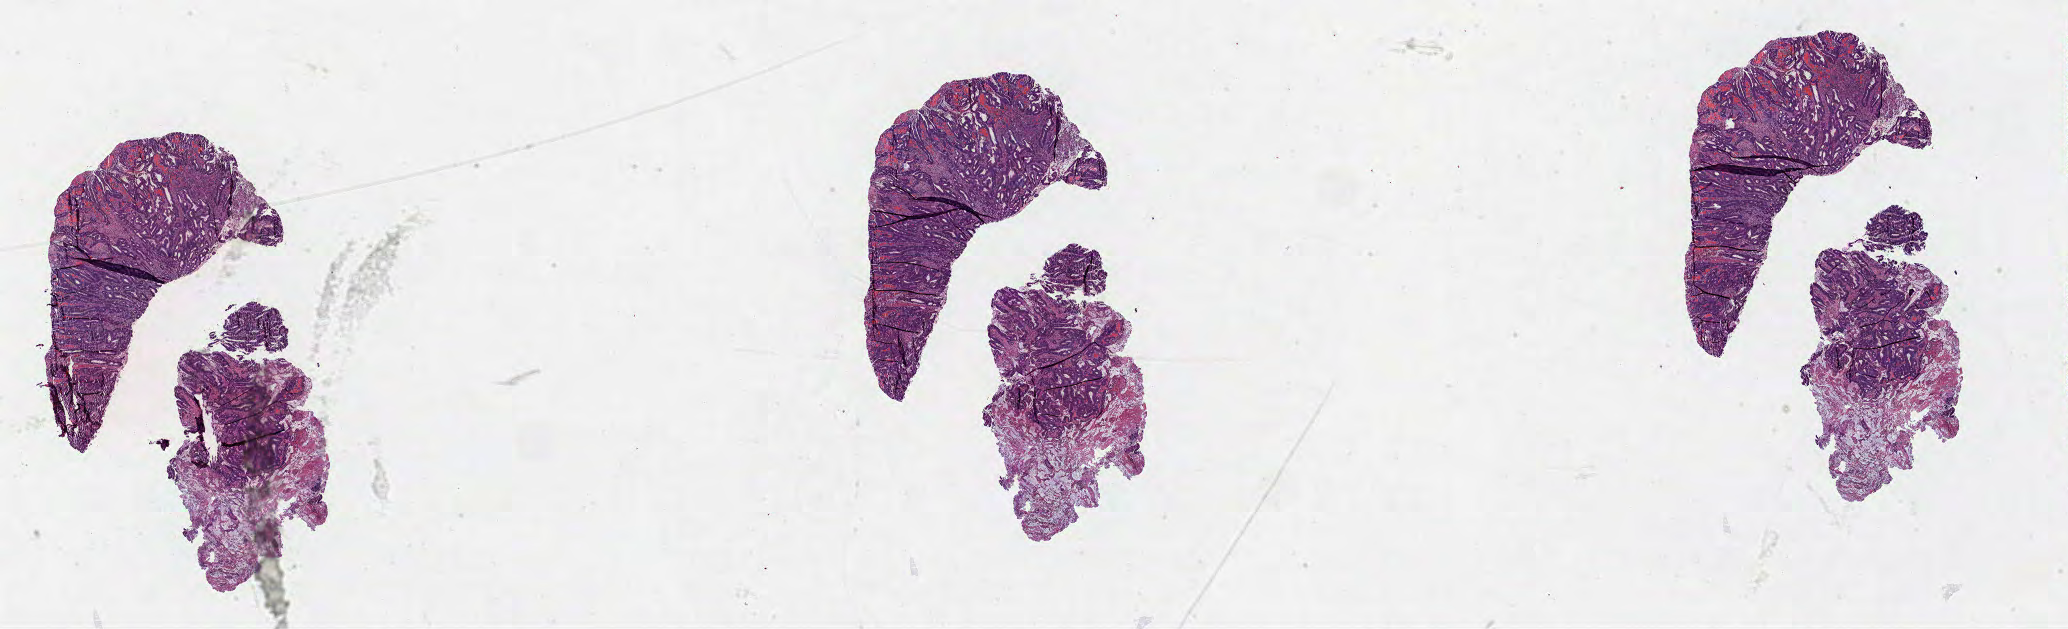
Hematoxylin and eosin (H&E) stained whole-slide image, a low-resolution overview of the entire scanned area, about 33.4 x 10.1 mm (from a 40x scan). Formalin-fixed paraffin-embedded (FFPE) diagnostic section. Sample: primary tumour, colon. Female patient; age at initial diagnosis 71 years.
- diagnosis: Mucinous adenocarcinoma
- lymph nodes positive (case pathology): 0 of 24 examined
- AJCC pathologic stage: IIB